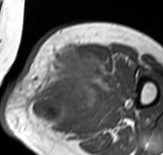
MRI of an extremity soft-tissue mass, one axial slice. Position 42 of 65 along the scan axis. MR volume resampled by the dataset authors to the PET/CT grid (not the native acquisition matrix). 3.27 mm slice thickness. 163 × 155 image matrix. Female patient. Case-level facts recorded for this patient, not image findings: histological type: pleomorphic leiomyosarcoma; grade: high; site of the primary tumour: left thigh.
Annotated regions visible in this slice (expert contour drawn on MRI and transferred to this co-registered scan by the dataset authors):
- gross tumour volume including surrounding oedema: bounding box [x1, y1, x2, y2] px = [28, 44, 107, 132]
- gross tumour volume (mass): [42, 44, 97, 121]